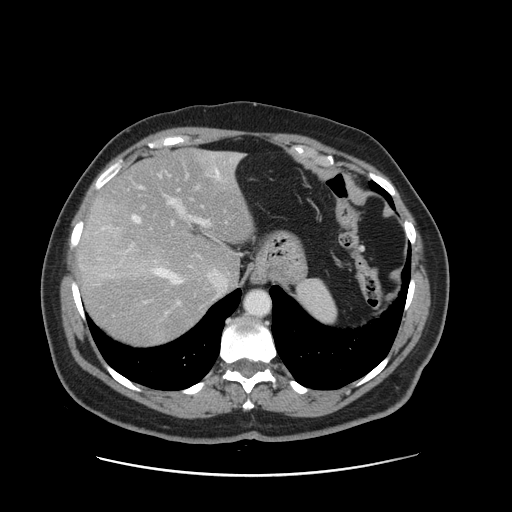
Contrast-enhanced abdominal CT, one axial slice. Position 115 of 161 along the scan axis. Intravenous contrast given. Soft-tissue window (W 400 / L 40 HU). 2.5 mm slice thickness. 512 × 512 image matrix, field of view 398 × 398 mm. Female patient, age 62 years. Case-level facts recorded for this patient, not image findings: diagnosis: colorectal cancer liver metastases, imaged before liver resection; multiple liver metastases: no; largest metastasis: 2.5 cm; chemotherapy before resection: yes.
Structures marked on this image (manually delineated by an expert):
- hepatic veins: box from (x=133, y=155) to (x=241, y=287) px
- liver: (x=78, y=149)–(x=255, y=348)
- planned liver remnant (the part of the liver to remain after resection): (x=96, y=149)–(x=255, y=283)
- portal vein (with intrahepatic branches): (x=162, y=170)–(x=210, y=305)